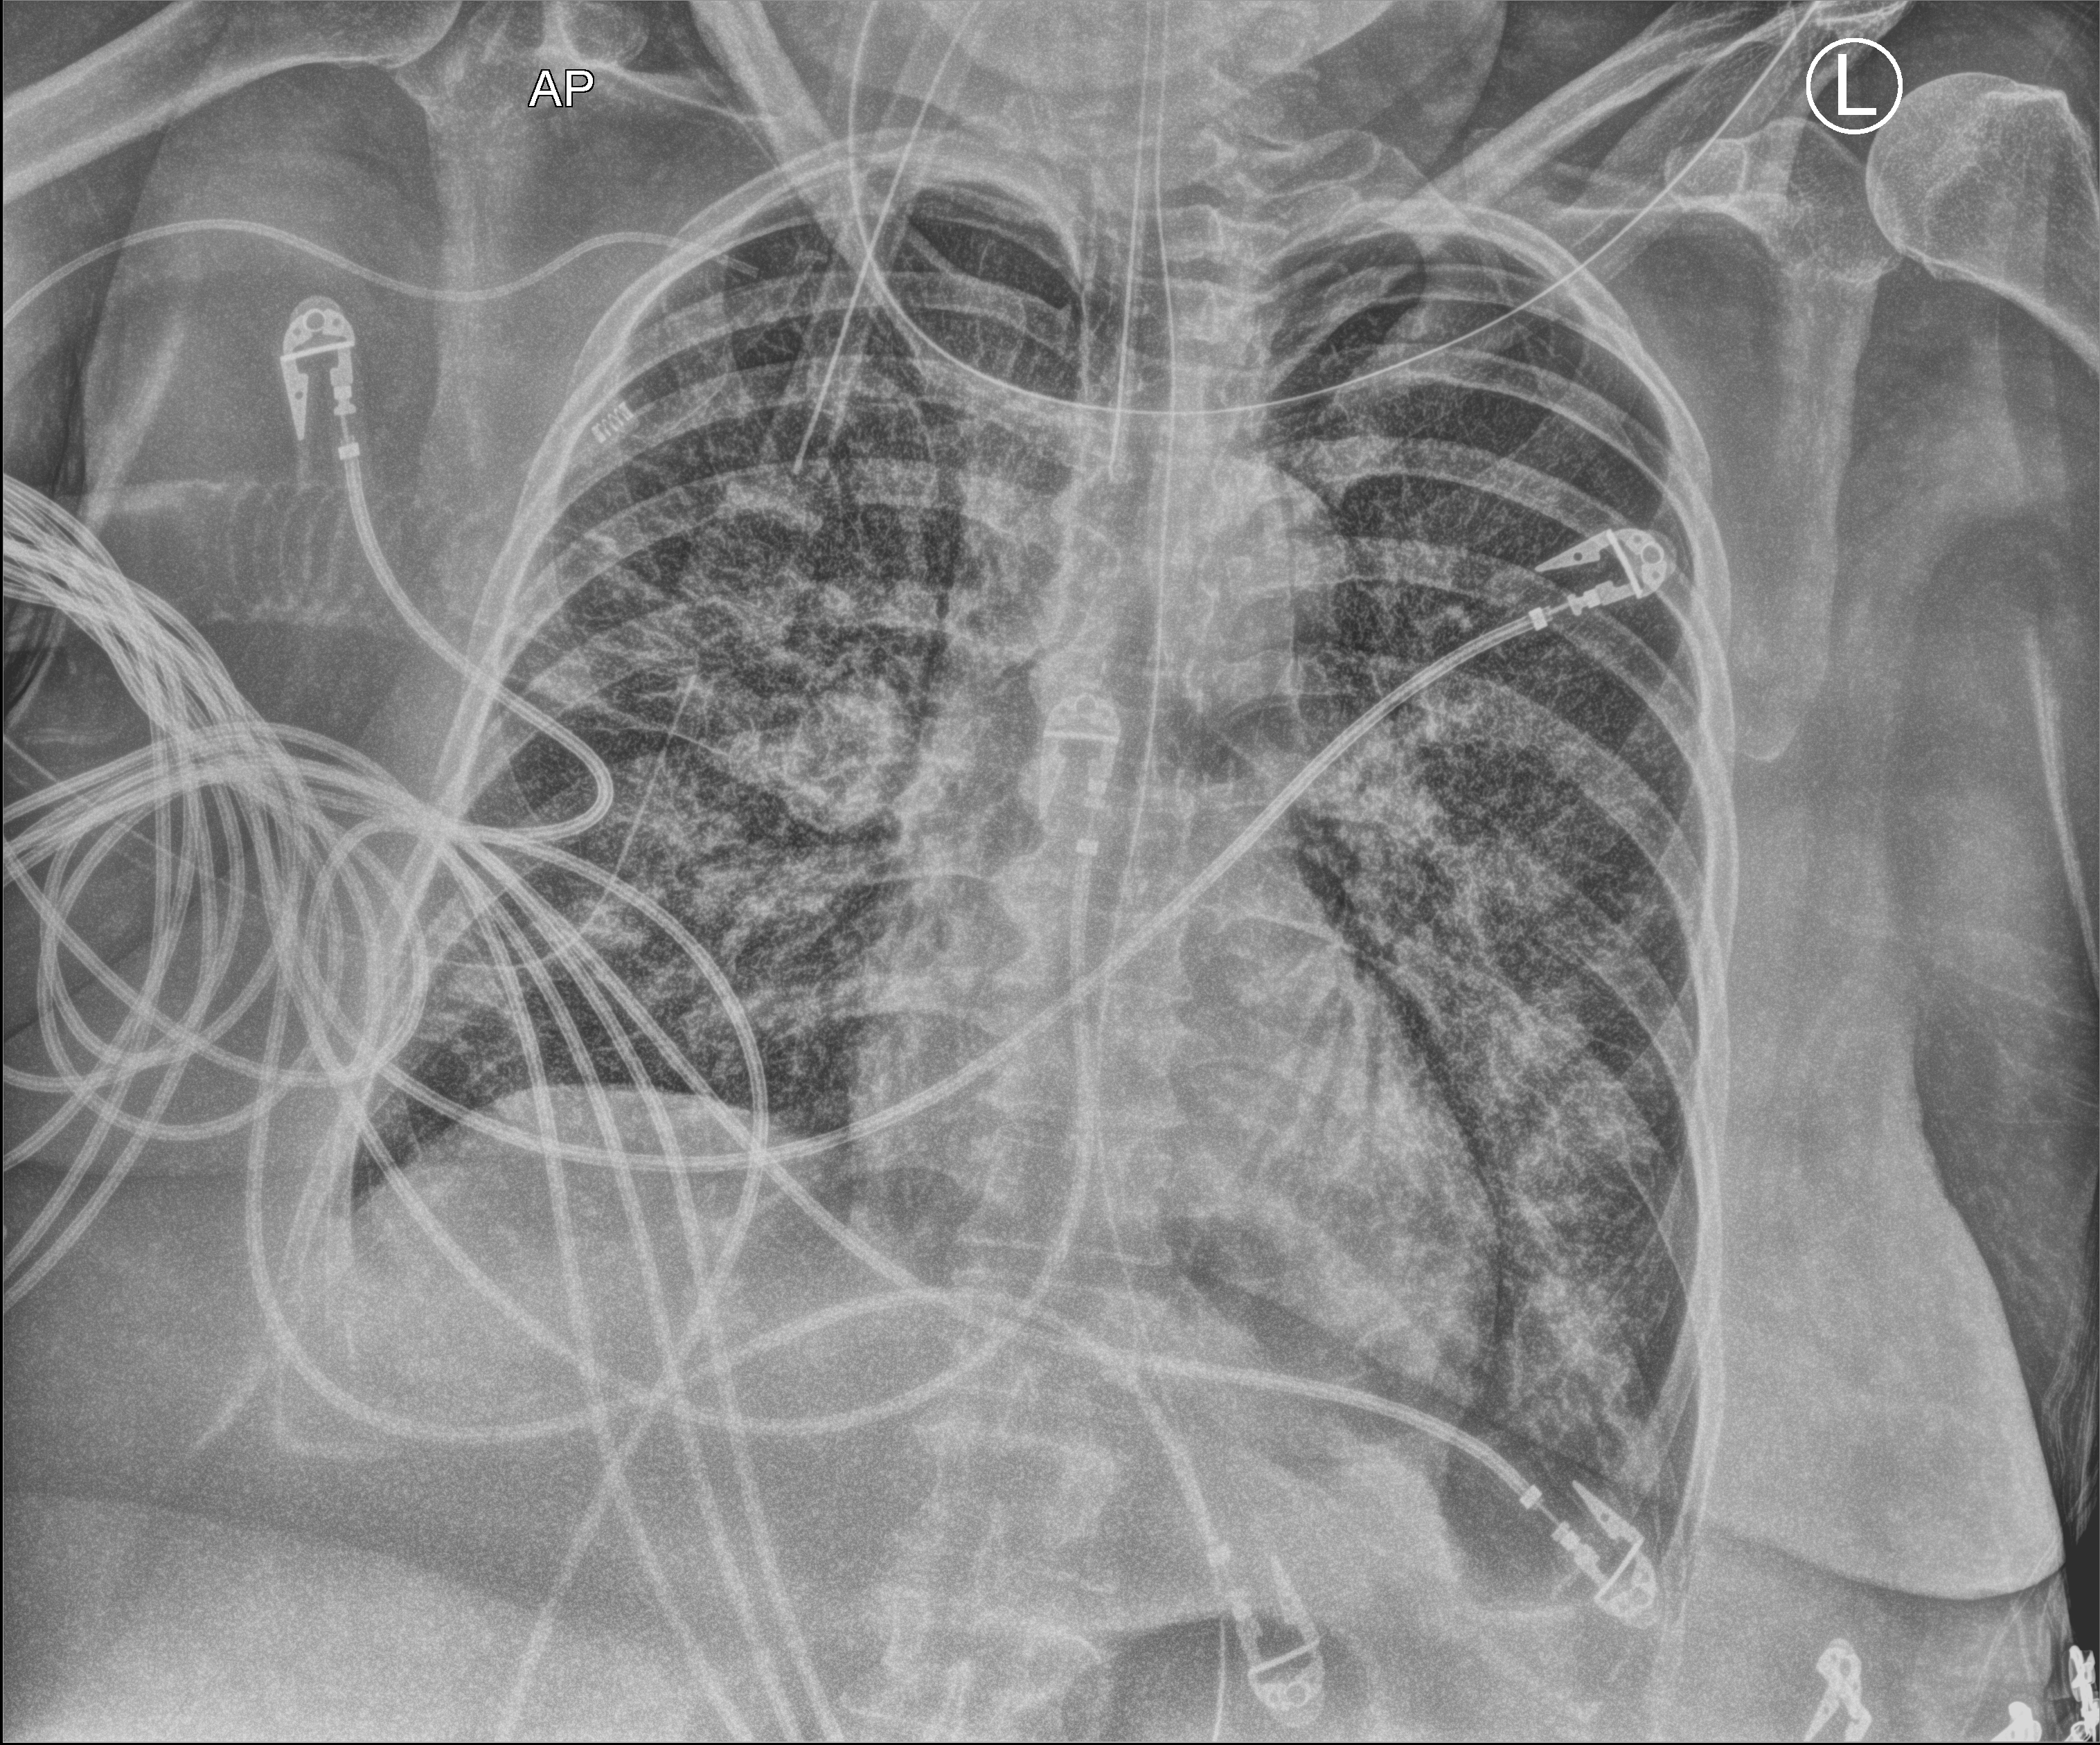
Bedside chest radiograph (computed radiography); anteroposterior (AP) projection. Patient hospitalised with COVID-19; female, aged 60–74 years.
Admission-level facts for this patient (not findings on this image; timing relative to this image not recorded): length of hospital stay: 38 days.